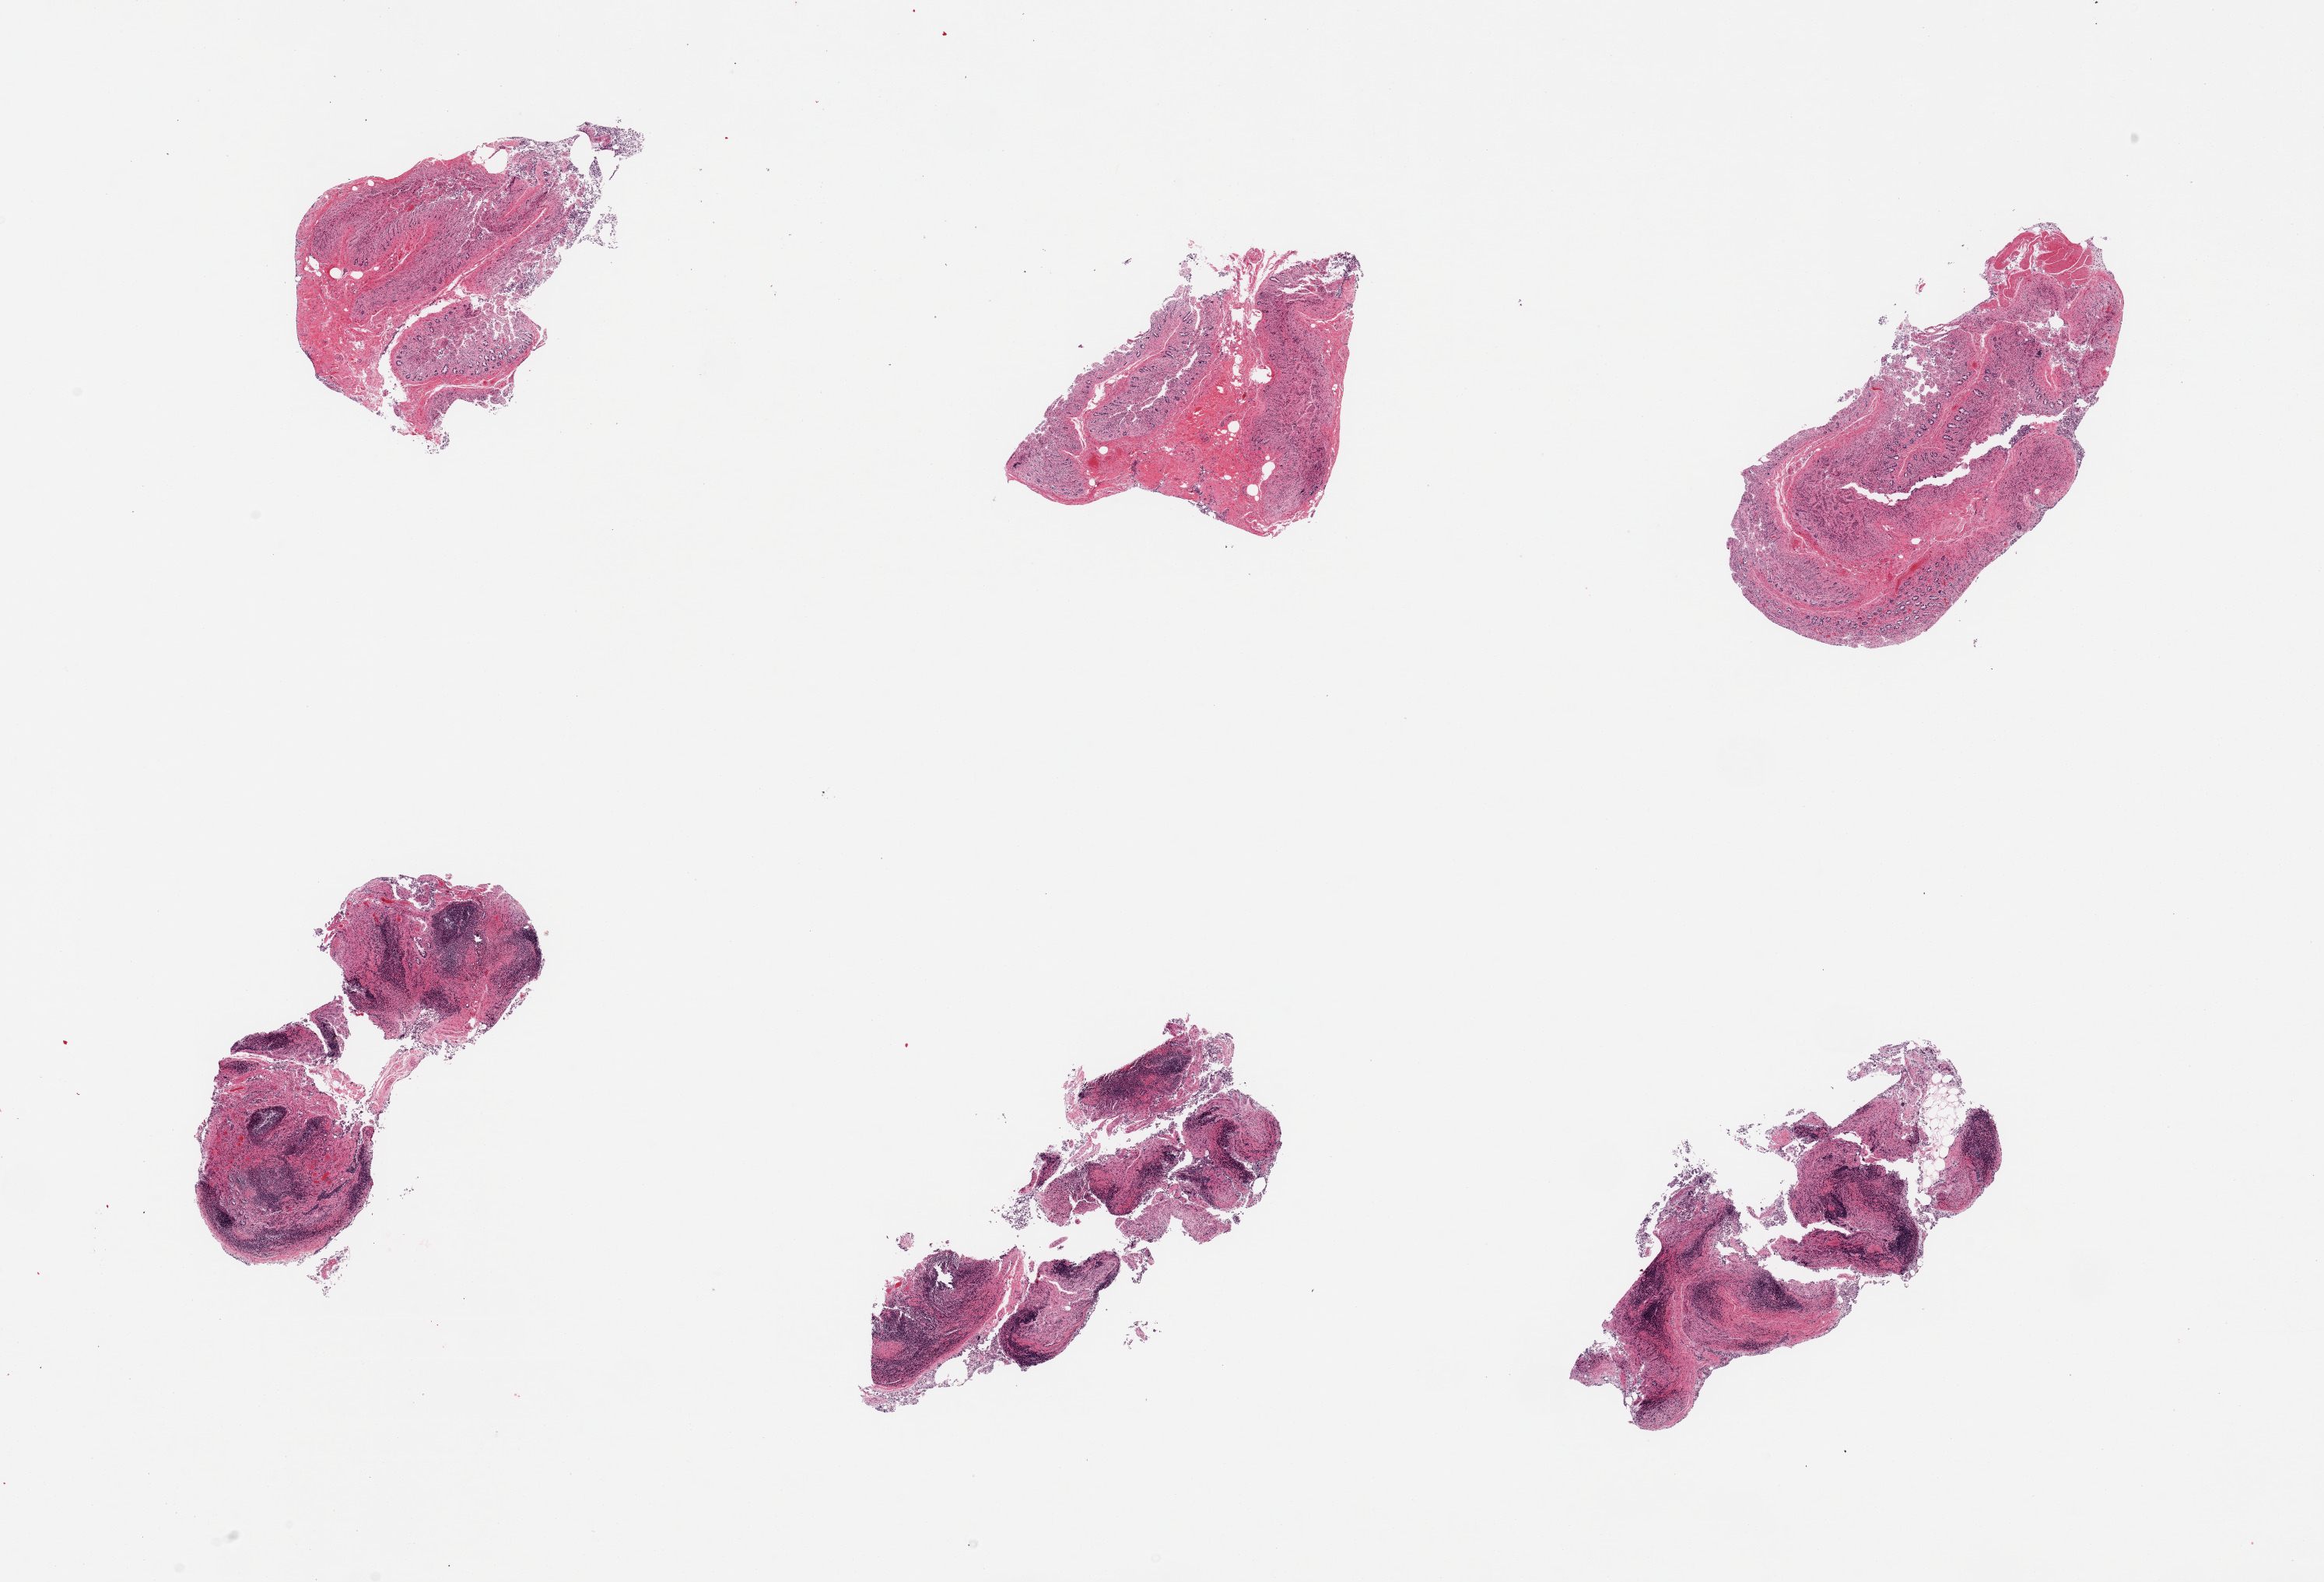
Whole-slide image, haematoxylin and eosin stain — low-resolution overview of the scanned area, about 23.6 x 16.1 mm. PAXgene-fixed, paraffin-embedded tissue. Section of ileum (target tissue). Donor tissue sample. Male donor.
Reviewer comment on this tissue sample: 6 pieces, glandular mucosa autolyzed, ~20% residual target lymphoid aggregates.